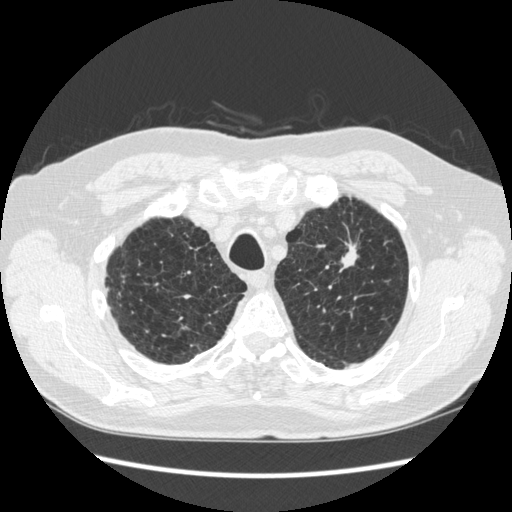
Low-dose screening chest CT, one axial slice; position 224 of 267 along the scan axis; 120 kVp; lung window (W 1500 / L -600 HU); 1.25 mm slice thickness; 512 × 512 image matrix.
Structures marked on this image (manually delineated by an expert):
- lesion 1 (tumor, upper lobe of left lung): box from (x=341, y=244) to (x=357, y=267) px